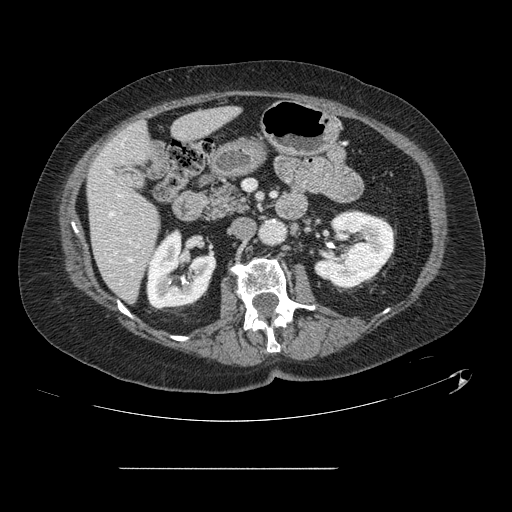
Contrast-enhanced abdominal CT, one axial slice; position 46 of 148 along the scan axis; intravenous contrast given; soft-tissue window (W 400 / L 40 HU); 512 × 512 image matrix, field of view 439 × 439 mm. Female patient, age 75 years. Case-level facts recorded for this patient, not image findings: diagnosis: colorectal cancer liver metastases, imaged before liver resection; multiple liver metastases: no; largest metastasis: 2.4 cm; disease in both lobes: no.
Outlined on this slice (expert manual segmentation):
- hepatic veins: bounding box <110,212,132,262> (left, top, right, bottom; pixels)
- liver: <88,108,237,301>
- planned liver remnant (the part of the liver to remain after resection): <88,108,236,301>